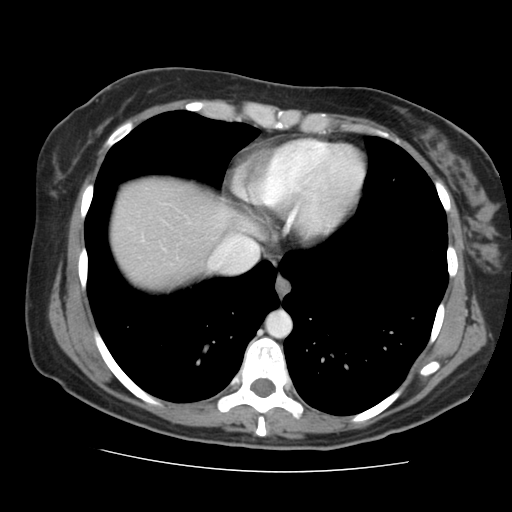
Contrast-enhanced abdominal CT, one axial slice; intravenous contrast given; soft-tissue window (W 400 / L 40 HU); 2.5 mm slice thickness; 512 × 512 image matrix. Female patient, age 46 years. Case-level facts recorded for this patient, not image findings: diagnosis: colorectal cancer liver metastases, imaged before liver resection; multiple liver metastases: no; largest metastasis: 2.8 cm; disease in both lobes: no.
Outlined on this slice (expert manual segmentation):
- hepatic veins: bounding box (x1, y1, x2, y2) in pixels: (209, 238, 259, 272)
- liver: (113, 179, 247, 288)
- planned liver remnant (the part of the liver to remain after resection): (113, 179, 247, 288)